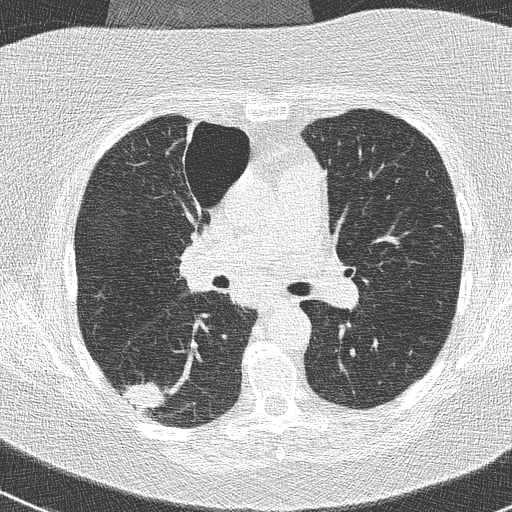
Low-dose screening chest CT, axial slice. Baseline screening round. Lung window (W 1500 / L -600 HU). Lung (sharp) reconstruction kernel (B50f). Slice 108 of 261 in the series. 512 × 512 image matrix. Female participant, aged 74 years at enrolment.
Expert-annotated lung lesion, bounding box <116,377,173,425> (left, top, right, bottom; pixels). The screening reader recorded 3 non-calcified nodules or masses ≥4 mm on this exam (right lower lobe, right upper lobe, left lower lobe); which of them this box marks is not recorded. Official screen result: positive, change unspecified: nodule(s) >= 4 mm or enlarging nodule(s), mass(es), or other non-specific abnormalities suspicious for lung cancer. Participant outcome: lung cancer diagnosed 16 days after this screen — non-small cell carcinoma, right lower lobe, poorly differentiated (G3), stage IIIA (AJCC 6th edition), 28 mm at pathology.